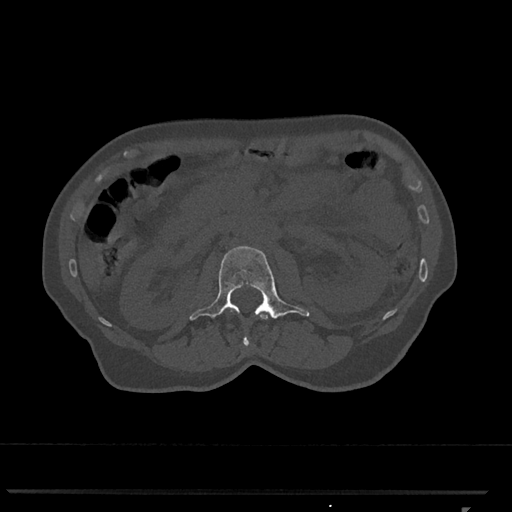
CT including the spine, one axial slice; reconstruction kernel Br40s/3; 120 kVp; bone window (W 1800 / L 400 HU); 0.5 mm slice thickness; 512 × 512 image matrix, field of view 380 × 380 mm. Patient: female, 62 years. From the clinical record (not read from this slice): primary cancer: renal.
Structures marked on this image (semi-automatically segmented with operator editing):
- L1 vertebra: bounding box [x1, y1, x2, y2] px = [231, 310, 268, 346]
- L2 vertebra: [189, 246, 310, 320]